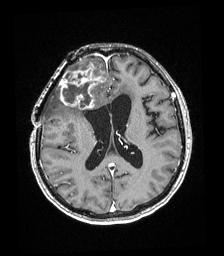
Brain MRI from a brain-tumour surgery series, one axial slice. Position 88 of 192 along the scan axis. T1-weighted post-contrast. 1 mm slice thickness. 224 × 256 image matrix, field of view 219 × 250 mm. From the clinical record (not read from this slice): histopathology: Astrocytoma; WHO grade: 4; IDH mutation: yes.
Structures marked on this image (manually delineated by an expert):
- tumour: bounding box (x1, y1, x2, y2) in pixels: (60, 65, 104, 109)